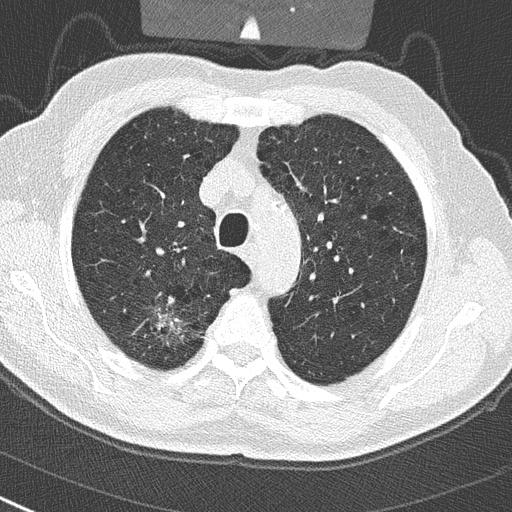
Chest CT (low-dose screening protocol), one axial image. Baseline screening round. Lung window (W 1500 / L -600 HU). Lung (sharp) reconstruction kernel (B50f). 120 kVp. Slice 70 of 290 in the series. 512 × 512 image matrix, field of view 300 × 300 mm. Male, age 65 years at enrolment.
- Expert reader's lesion annotation, bounding box (x1, y1, x2, y2) in pixels: (130, 299, 198, 360).
- Reader record for this screening exam (exam-level; its link to the box is not recorded): non-calcified nodule or mass ≥4 mm, right upper lobe, 24 × 19 mm, spiculated (stellate) margins, soft tissue attenuation.
- Lung cancer was diagnosed 32 days after this screen: non-small cell carcinoma, right upper lobe, poorly differentiated (G3), stage IA (AJCC 6th edition), 29 mm at pathology.